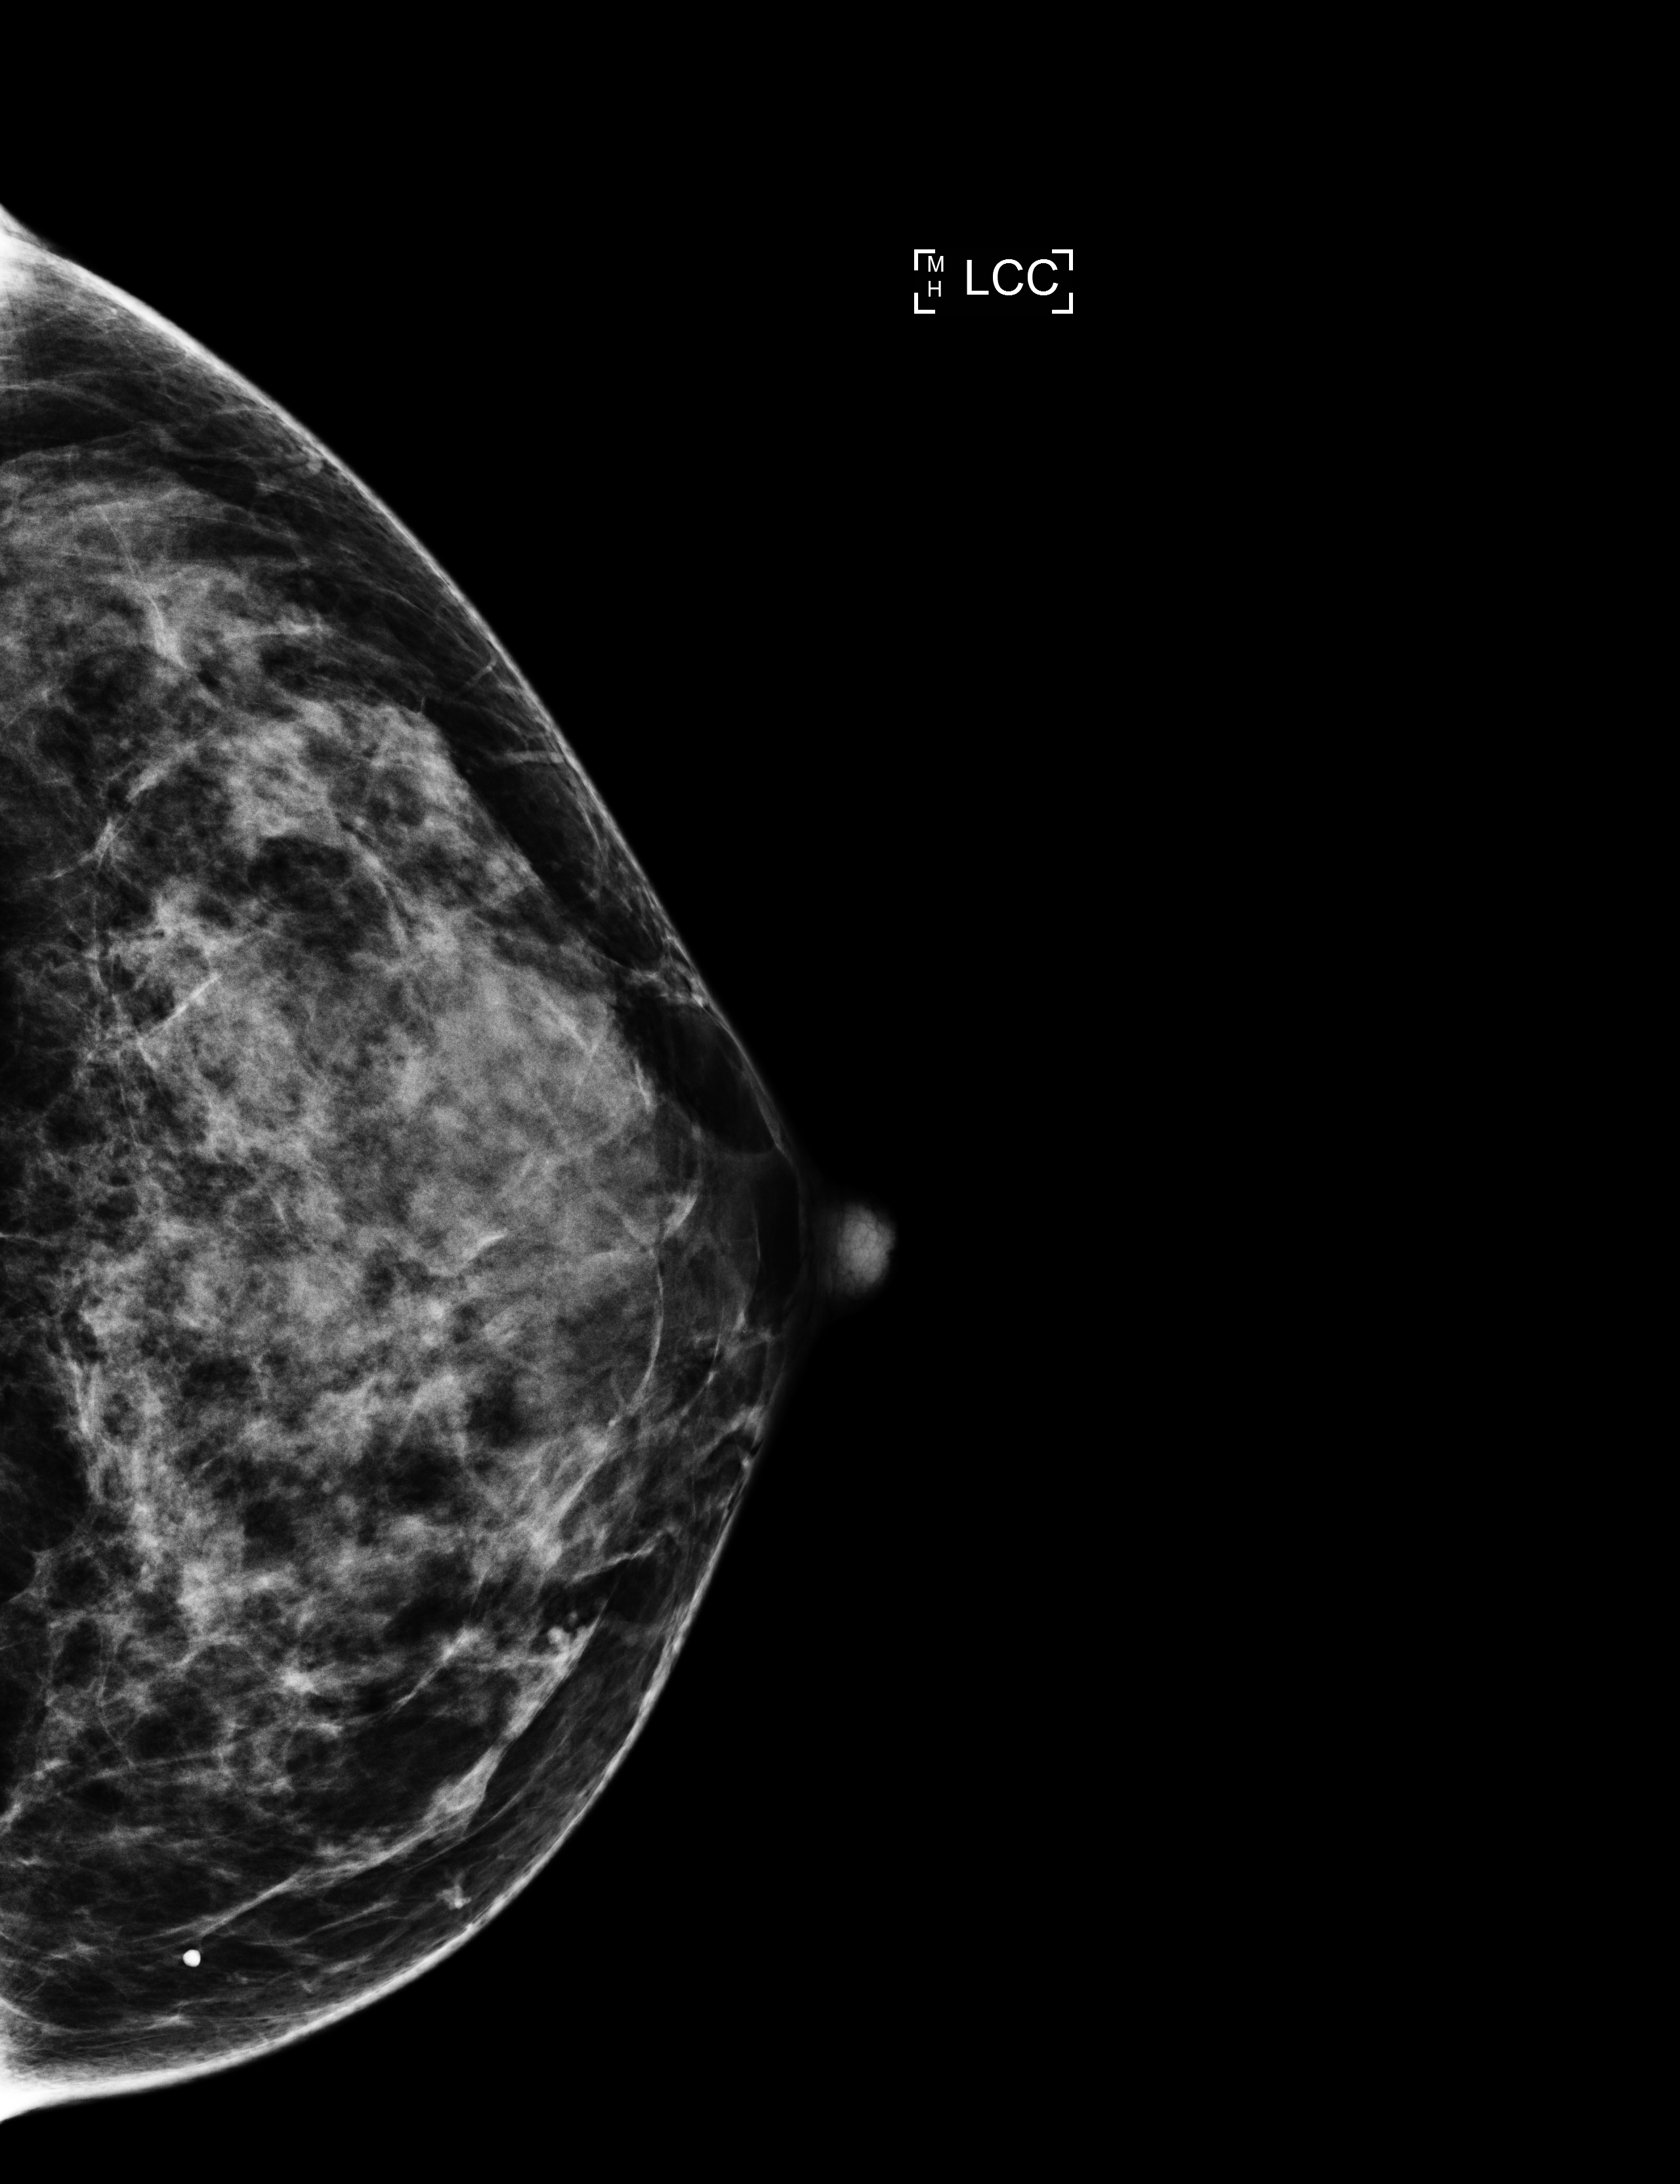
Full-field digital mammogram (FFDM), left breast, CC view, annual screening mammography examination, system: Selenia Dimensions. Female patient, age 41 years.
Breast density at the screening exam (both breasts): extremely dense (BI-RADS density category d). Final BI-RADS category for the screening round (tomosynthesis exam, both breasts): category 1. Recall: no recall after this screen.